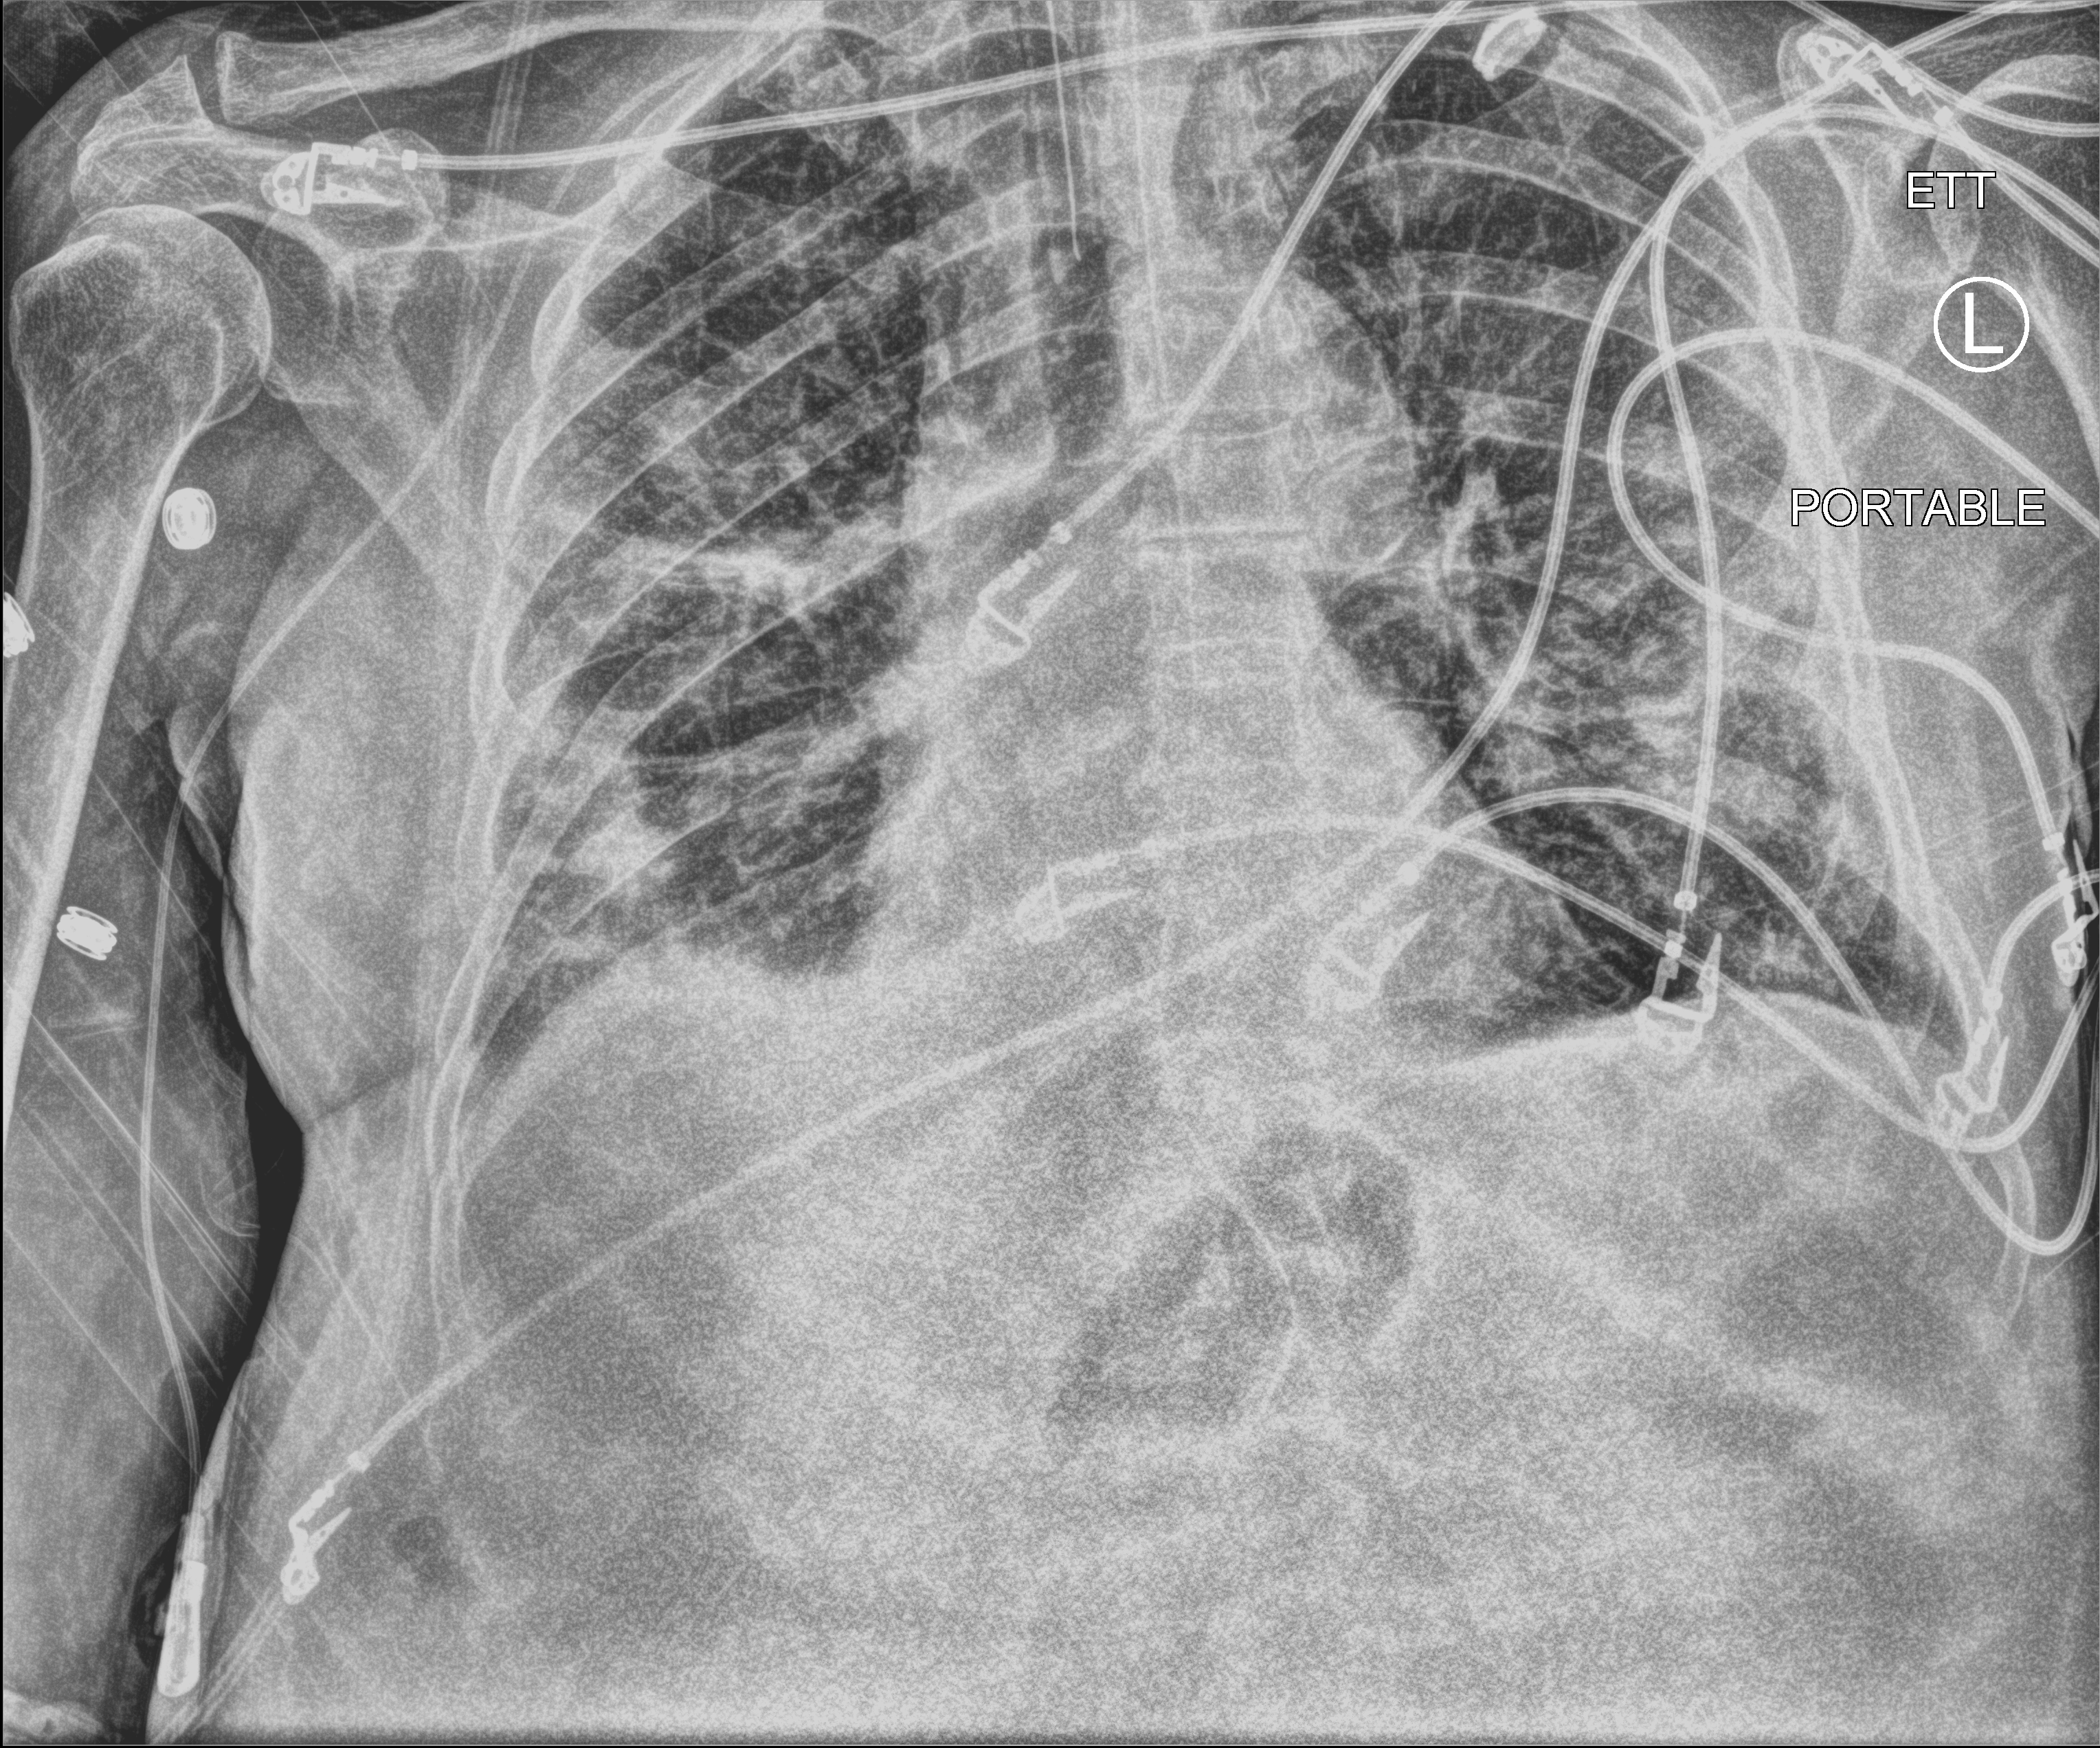
Bedside chest radiograph (computed radiography); anteroposterior (AP) projection. Male patient hospitalised with COVID-19, age 75–90 years.
Admission-level facts for this patient (not findings on this image; timing relative to this image not recorded): admitted to intensive care during this hospital stay: yes.